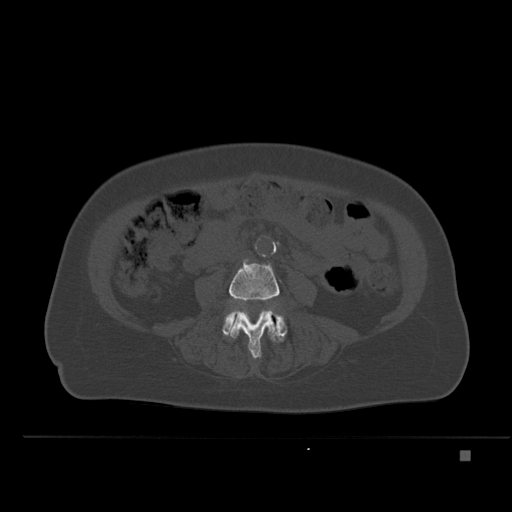
CT including the spine, one axial slice; position 175 of 477 along the scan axis; bone window (W 1800 / L 400 HU); 512 × 512 image matrix, field of view 422 × 422 mm. Female patient, age 74 years. From the clinical record (not read from this slice): primary cancer: colon.
Annotated regions visible in this slice (semi-automatic segmentation, software-assisted and operator-edited):
- L4 vertebra: box from (x=229, y=258) to (x=280, y=359) px
- L5 vertebra: (x=222, y=307)–(x=287, y=343)